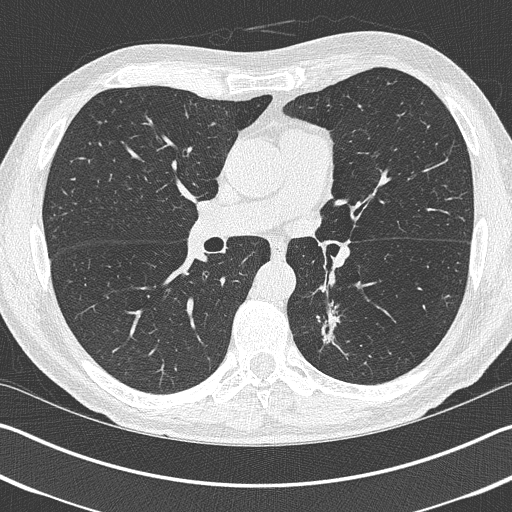
Low-dose screening chest CT, one axial slice. Slice 228 of 402 in the series (ordered by position). Reconstruction kernel B50f. Lung window (W 1500 / L -600 HU). 1 mm slice thickness. 512 × 512 image matrix, field of view 340 × 340 mm.
Annotated regions visible in this slice (outlined manually by an expert reader):
- lesion 1 (tumor, lower lobe of left lung): box from (x=317, y=302) to (x=340, y=343) px